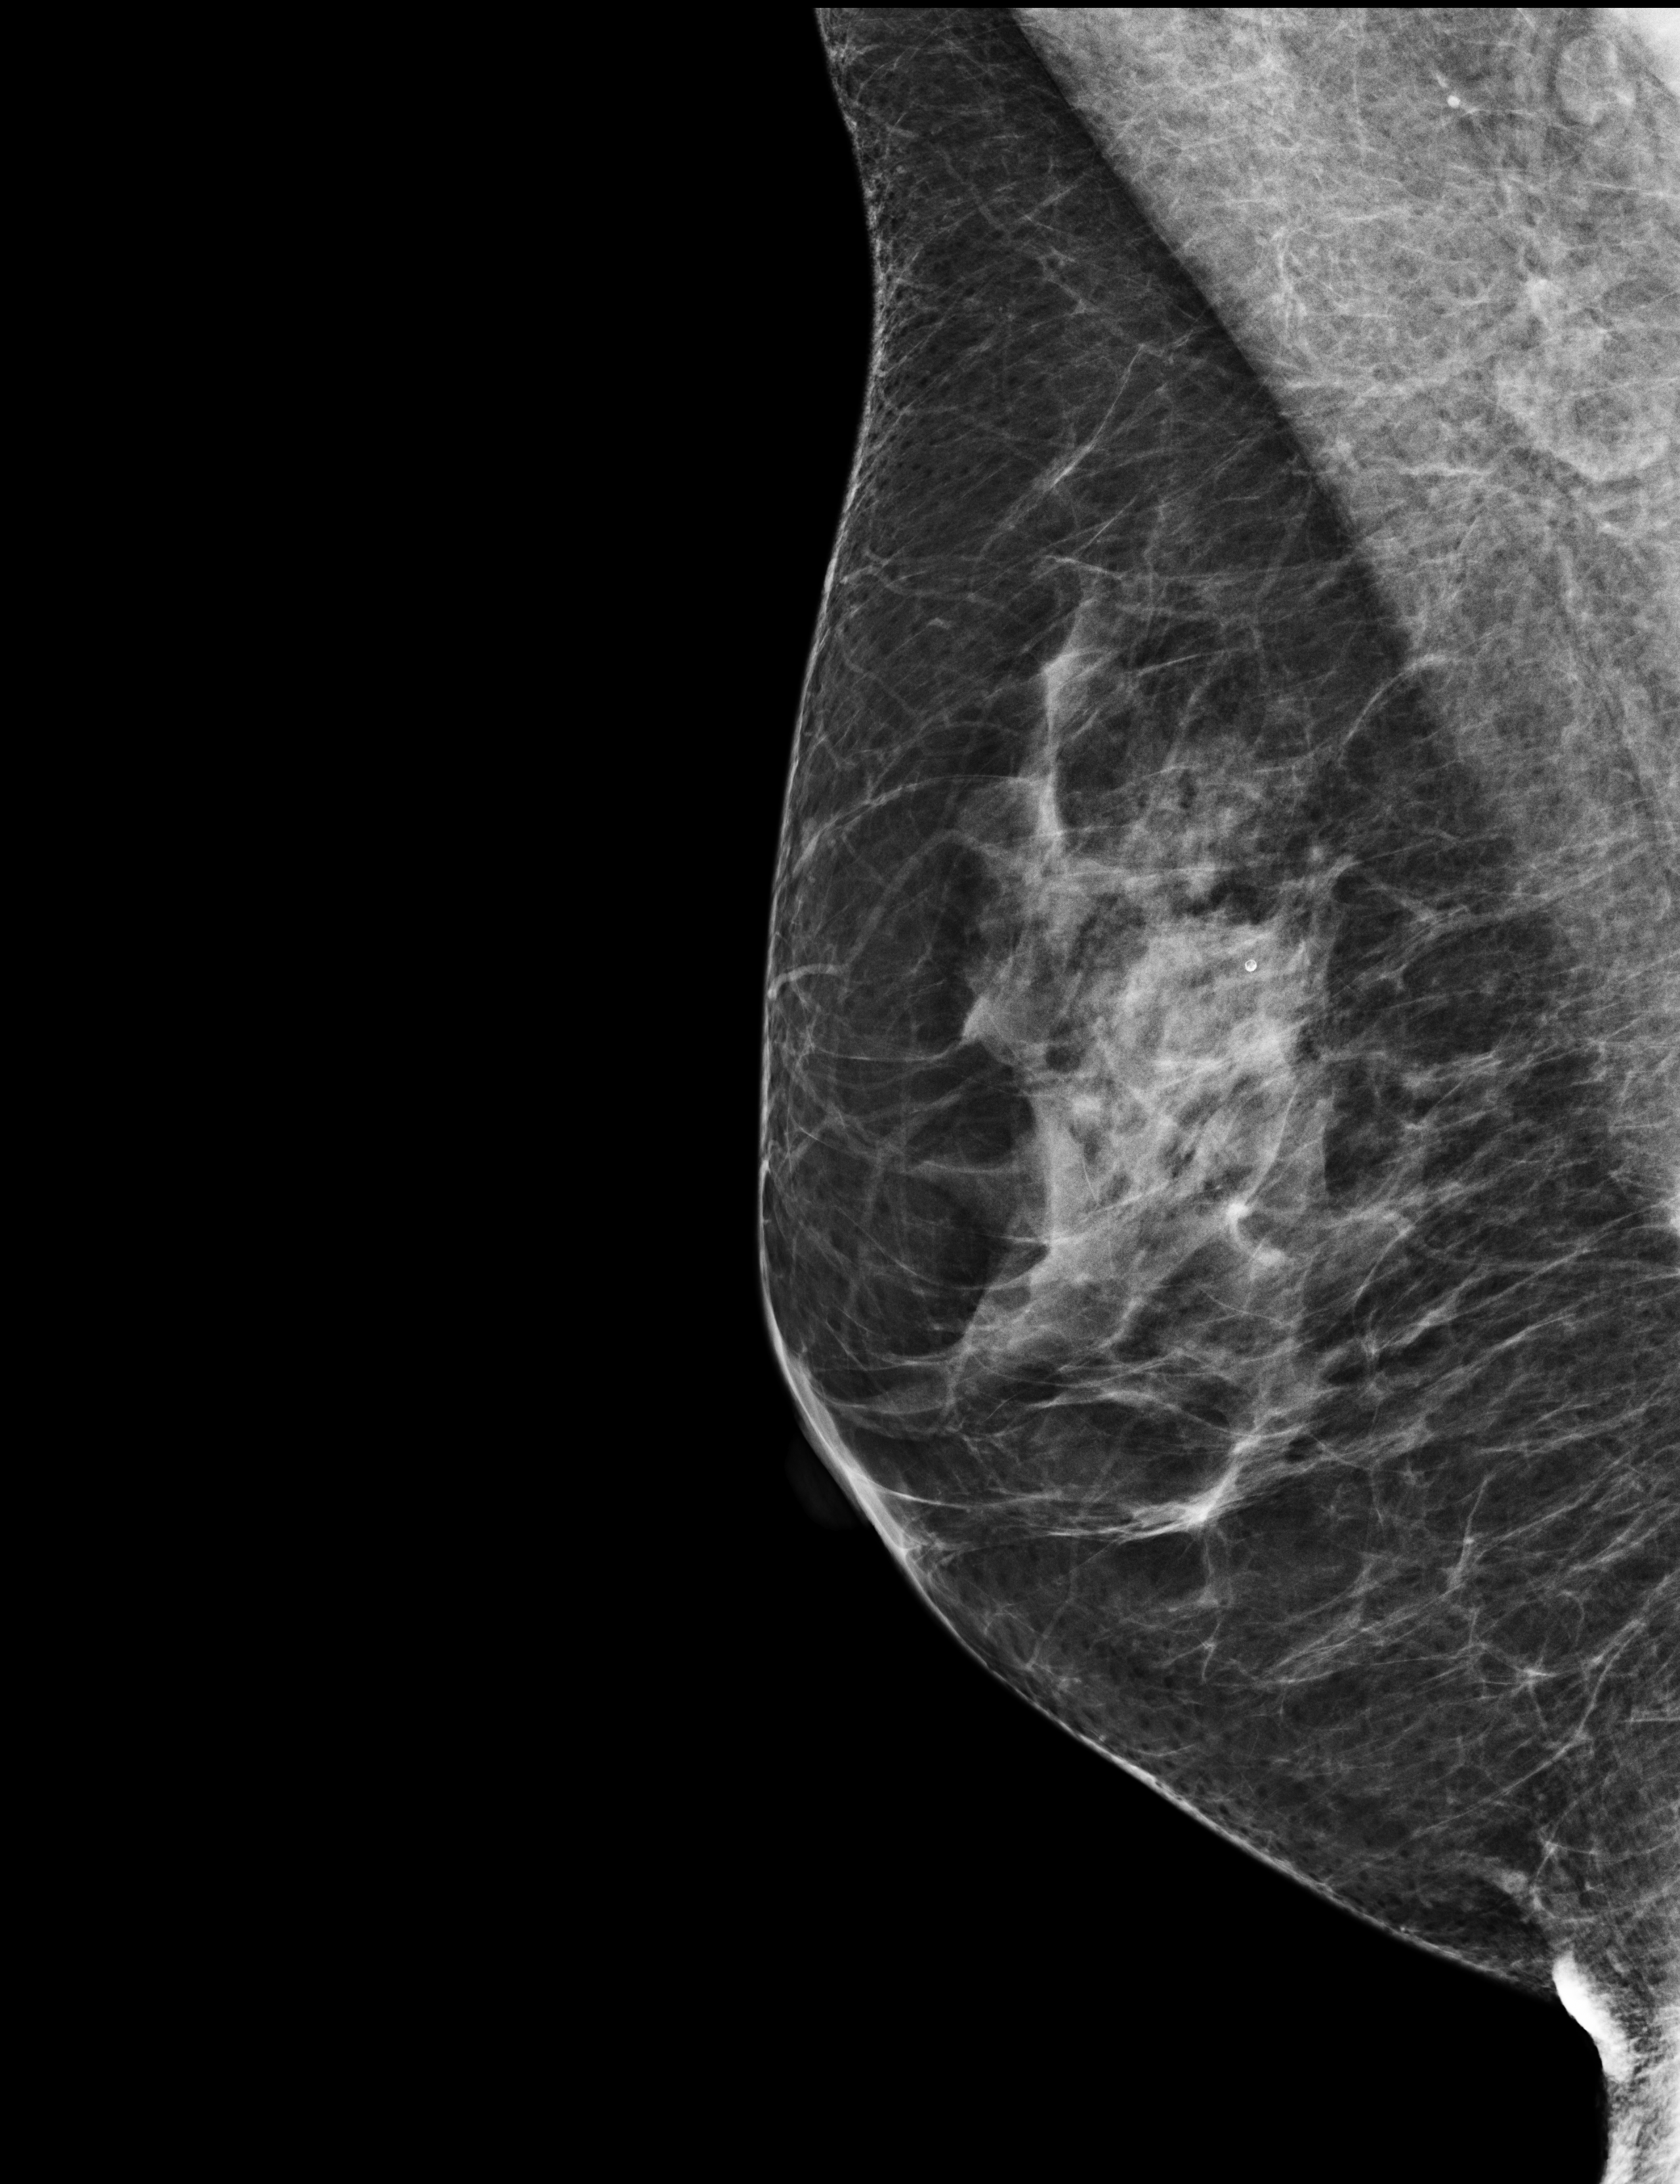
Annual screening mammography examination, compressed breast thickness 66 mm. Female patient, age 63 years.
Image type: full-field digital mammogram. Breast: right. Projection: mediolateral oblique (MLO) view. BI-RADS breast density category at the screening exam (both breasts, scale 1–4): 3. Final BI-RADS category for the screening round (tomosynthesis exam, both breasts): category 1. Recall: no recall after this screen.